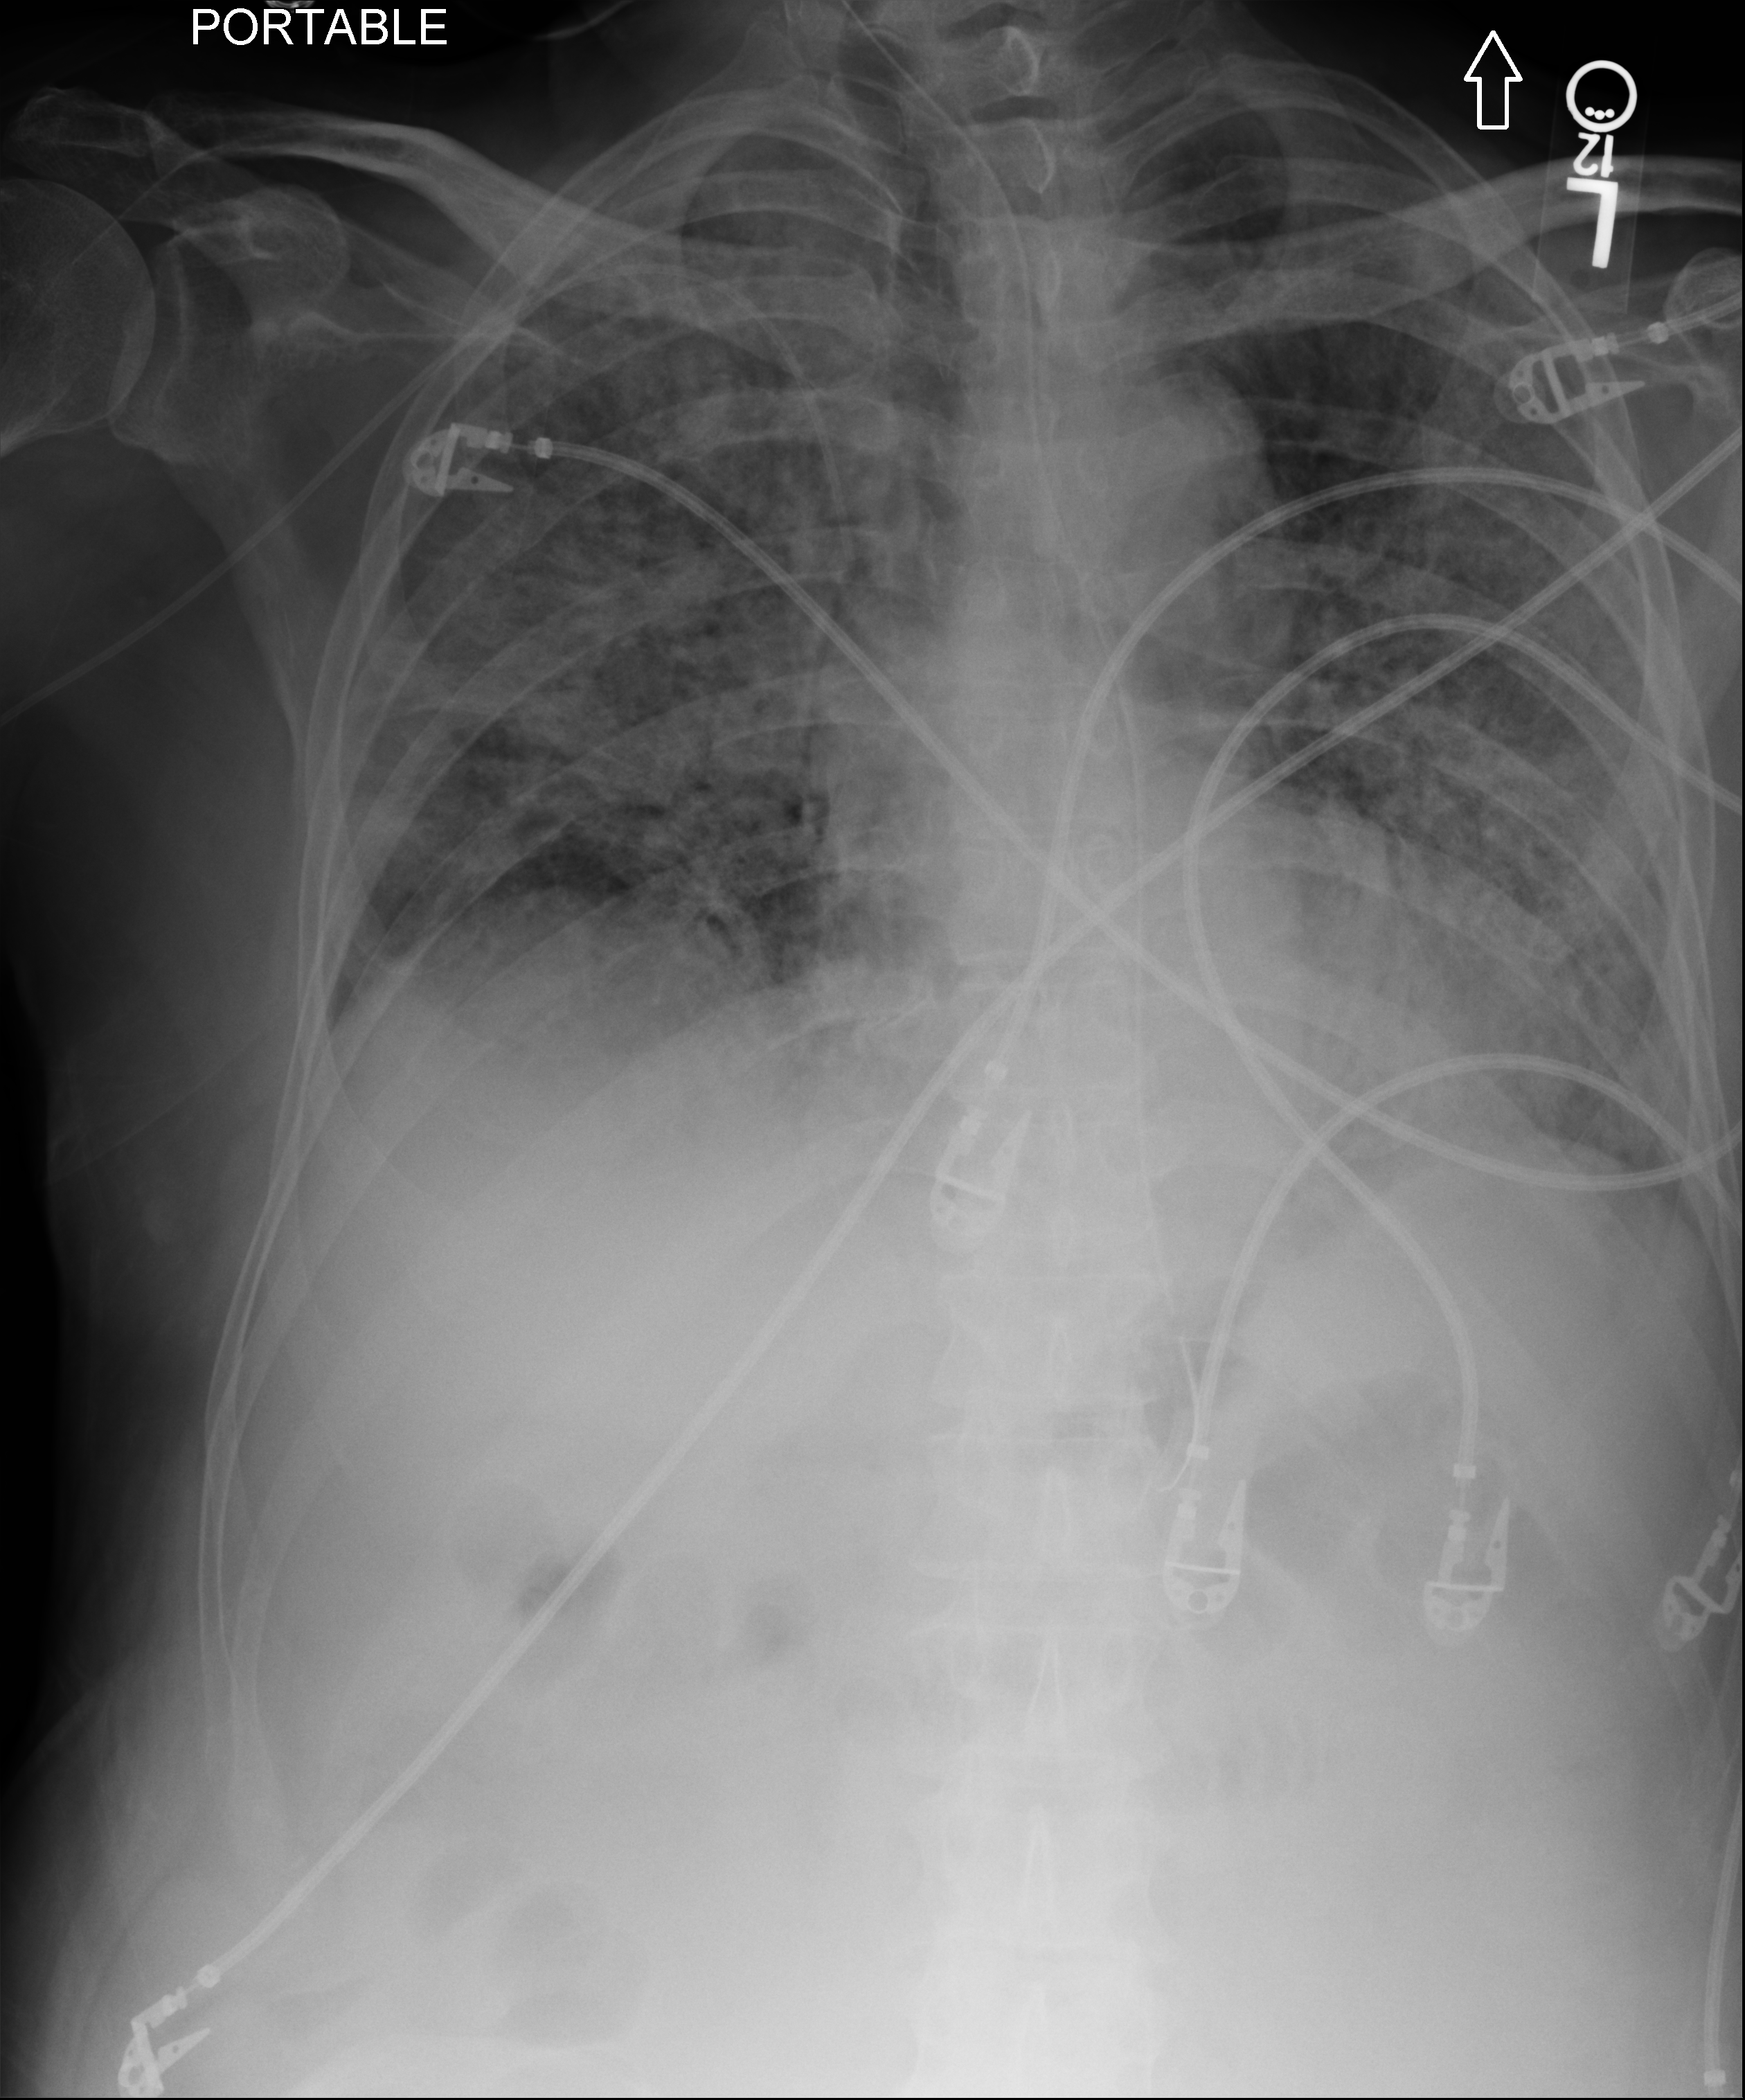
Bedside chest radiograph (computed radiography); anteroposterior (AP) projection. Patient hospitalised with COVID-19; male, aged 60–74 years.
Hospital-stay facts (about this admission, not read from this image; timing relative to this image not recorded):
- length of hospital stay: 28 days
- mechanically ventilated during this hospital stay: yes
- admitted to intensive care during this hospital stay: yes